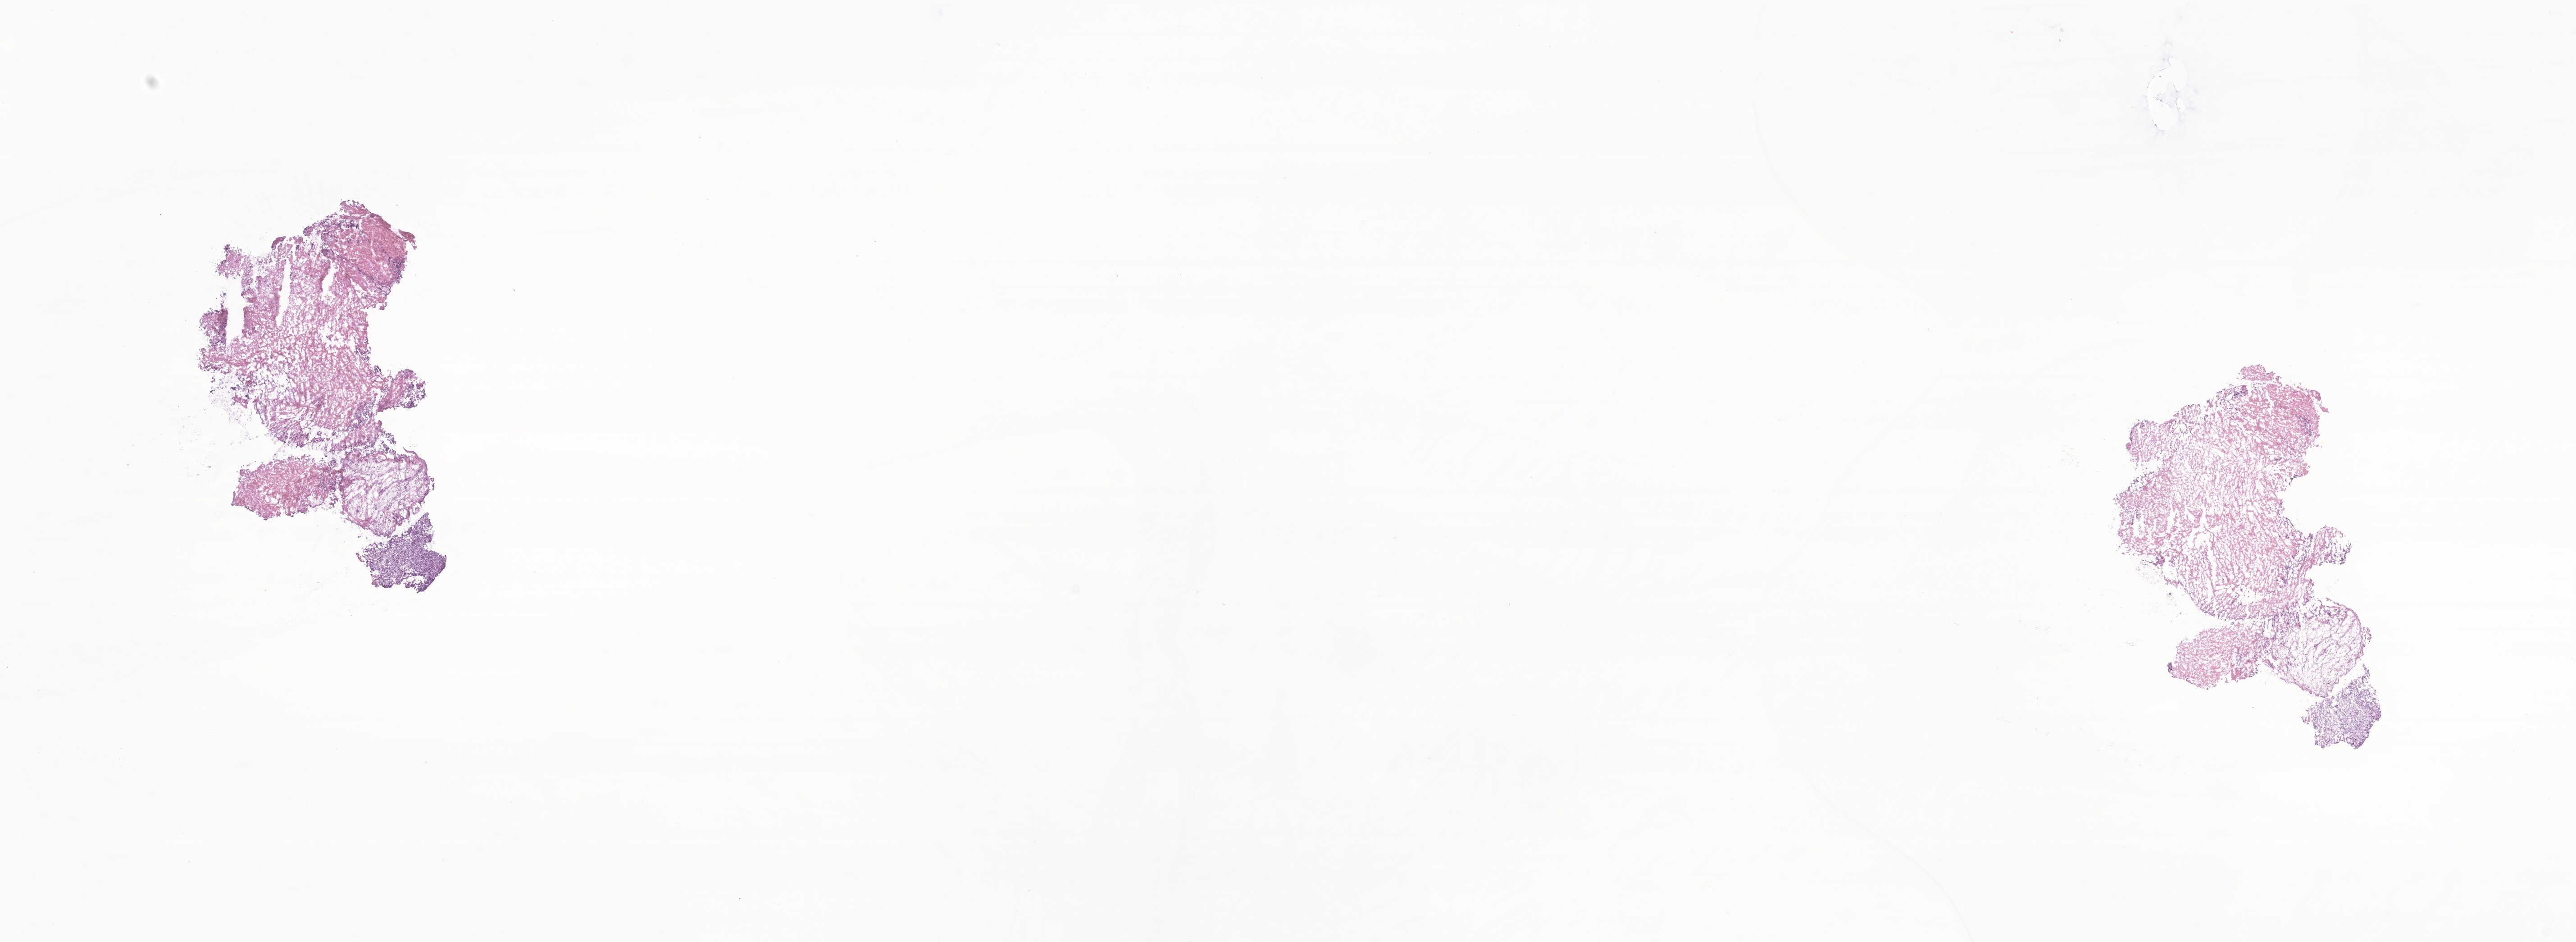
Whole-slide image, hematoxylin and eosin (H&E) stain of tumor tissue from the brain, low-resolution overview of the scanned area, about 24.1 x 8.8 mm; frozen section (OCT-embedded). Patient: female, age 97 months (8 years 1 month).
Diagnosis (ICD-O-3 morphology term): Dysgerminoma.